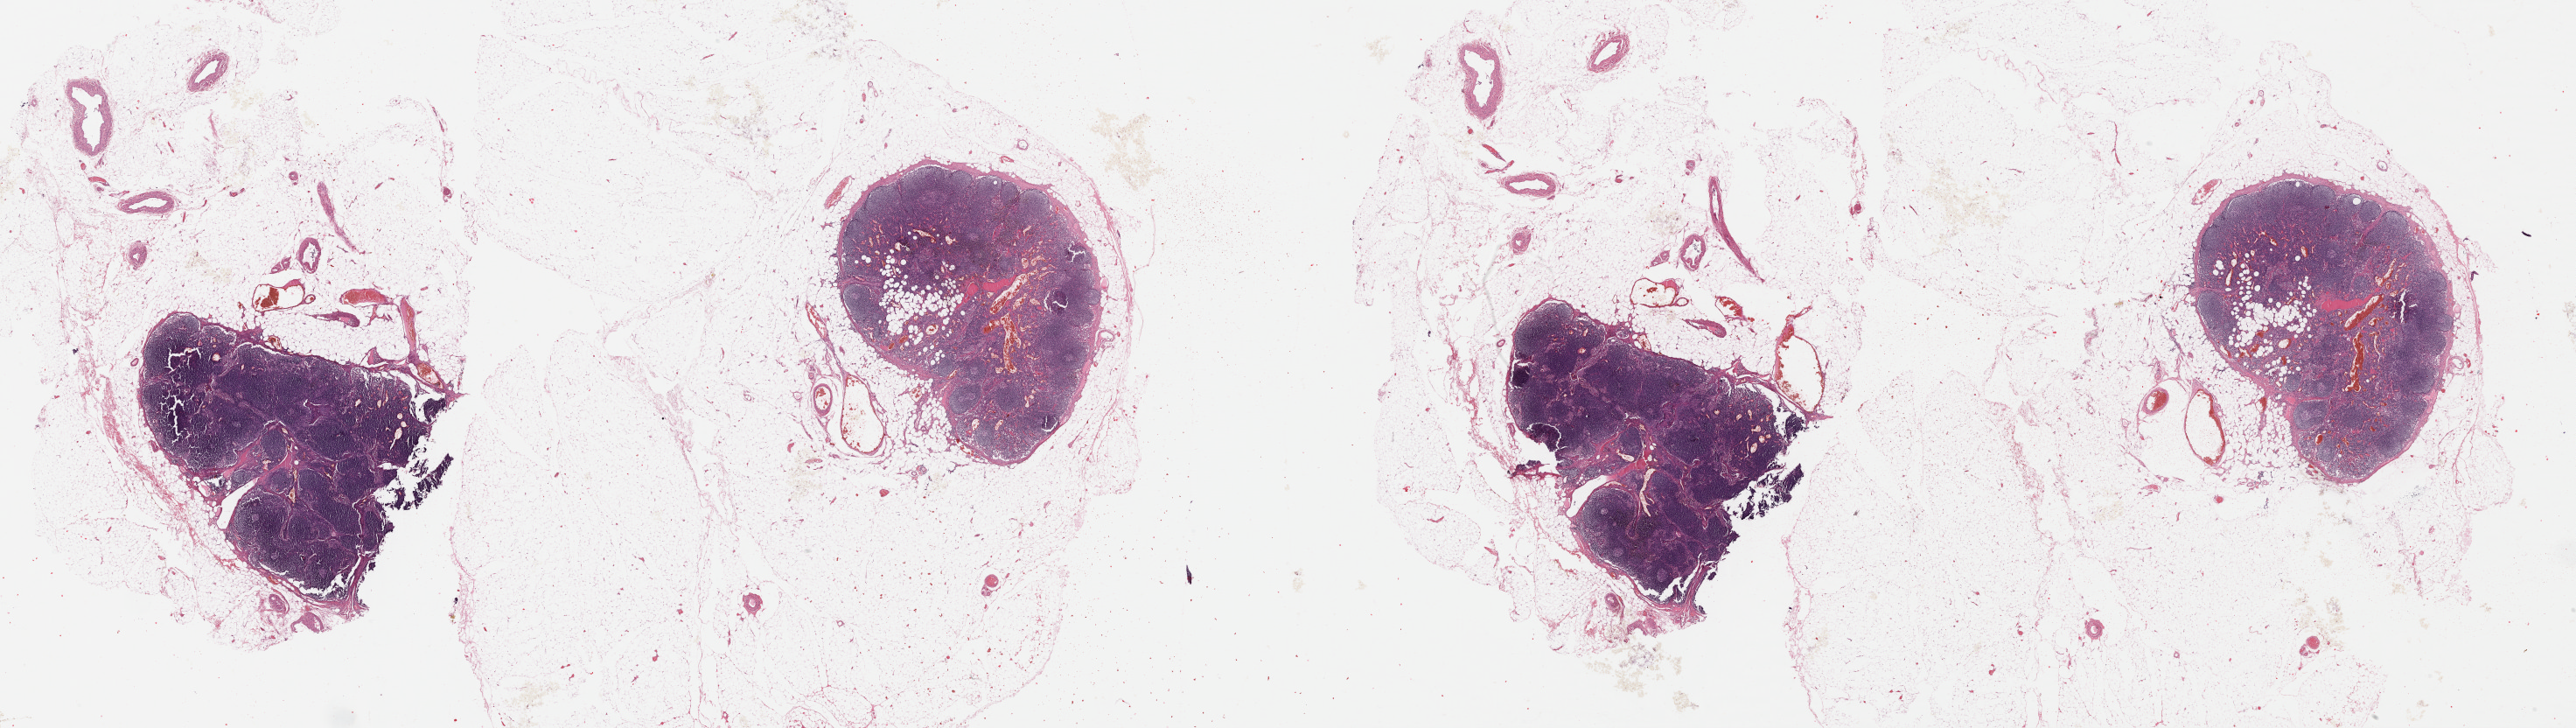
Whole-slide histology image, Hematoxylin and eosin (H&E) stained — a low-resolution overview of the entire scanned area, about 46.3 x 13.1 mm (acquisition: 40x scan). Formalin-fixed paraffin-embedded (FFPE) diagnostic section. Metastatic tumour sample, sampled site: lymph node. Male, age 65 years at initial diagnosis.
- this section: metastatic tumour tissue
- patient diagnosis: Malignant melanoma, NOS